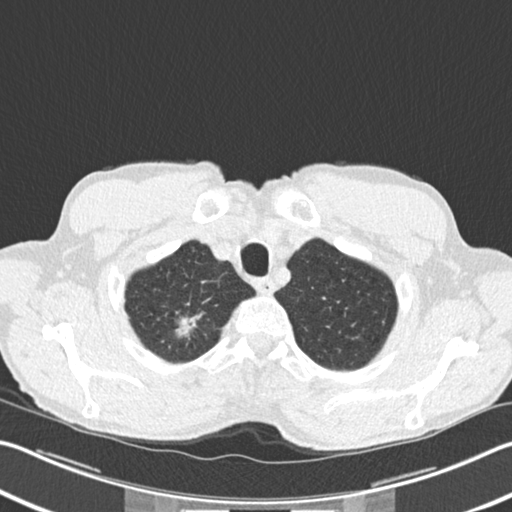
Chest CT (low-dose screening protocol), one axial image, second annual screen, lung window (W 1500 / L -600 HU), standard (soft-tissue) reconstruction kernel (B30f), slice 23 of 220 in the series. Male, age 62 years at enrolment. Former smoker at enrolment.
Expert-annotated lung lesion, bounding box (x1, y1, x2, y2) in pixels: (164, 302, 208, 346). The screening reader recorded 2 non-calcified nodules or masses ≥4 mm on this exam; which of them this box marks is not recorded. Official screen result: positive, change unspecified: nodule(s) >= 4 mm or enlarging nodule(s), mass(es), or other non-specific abnormalities suspicious for lung cancer.